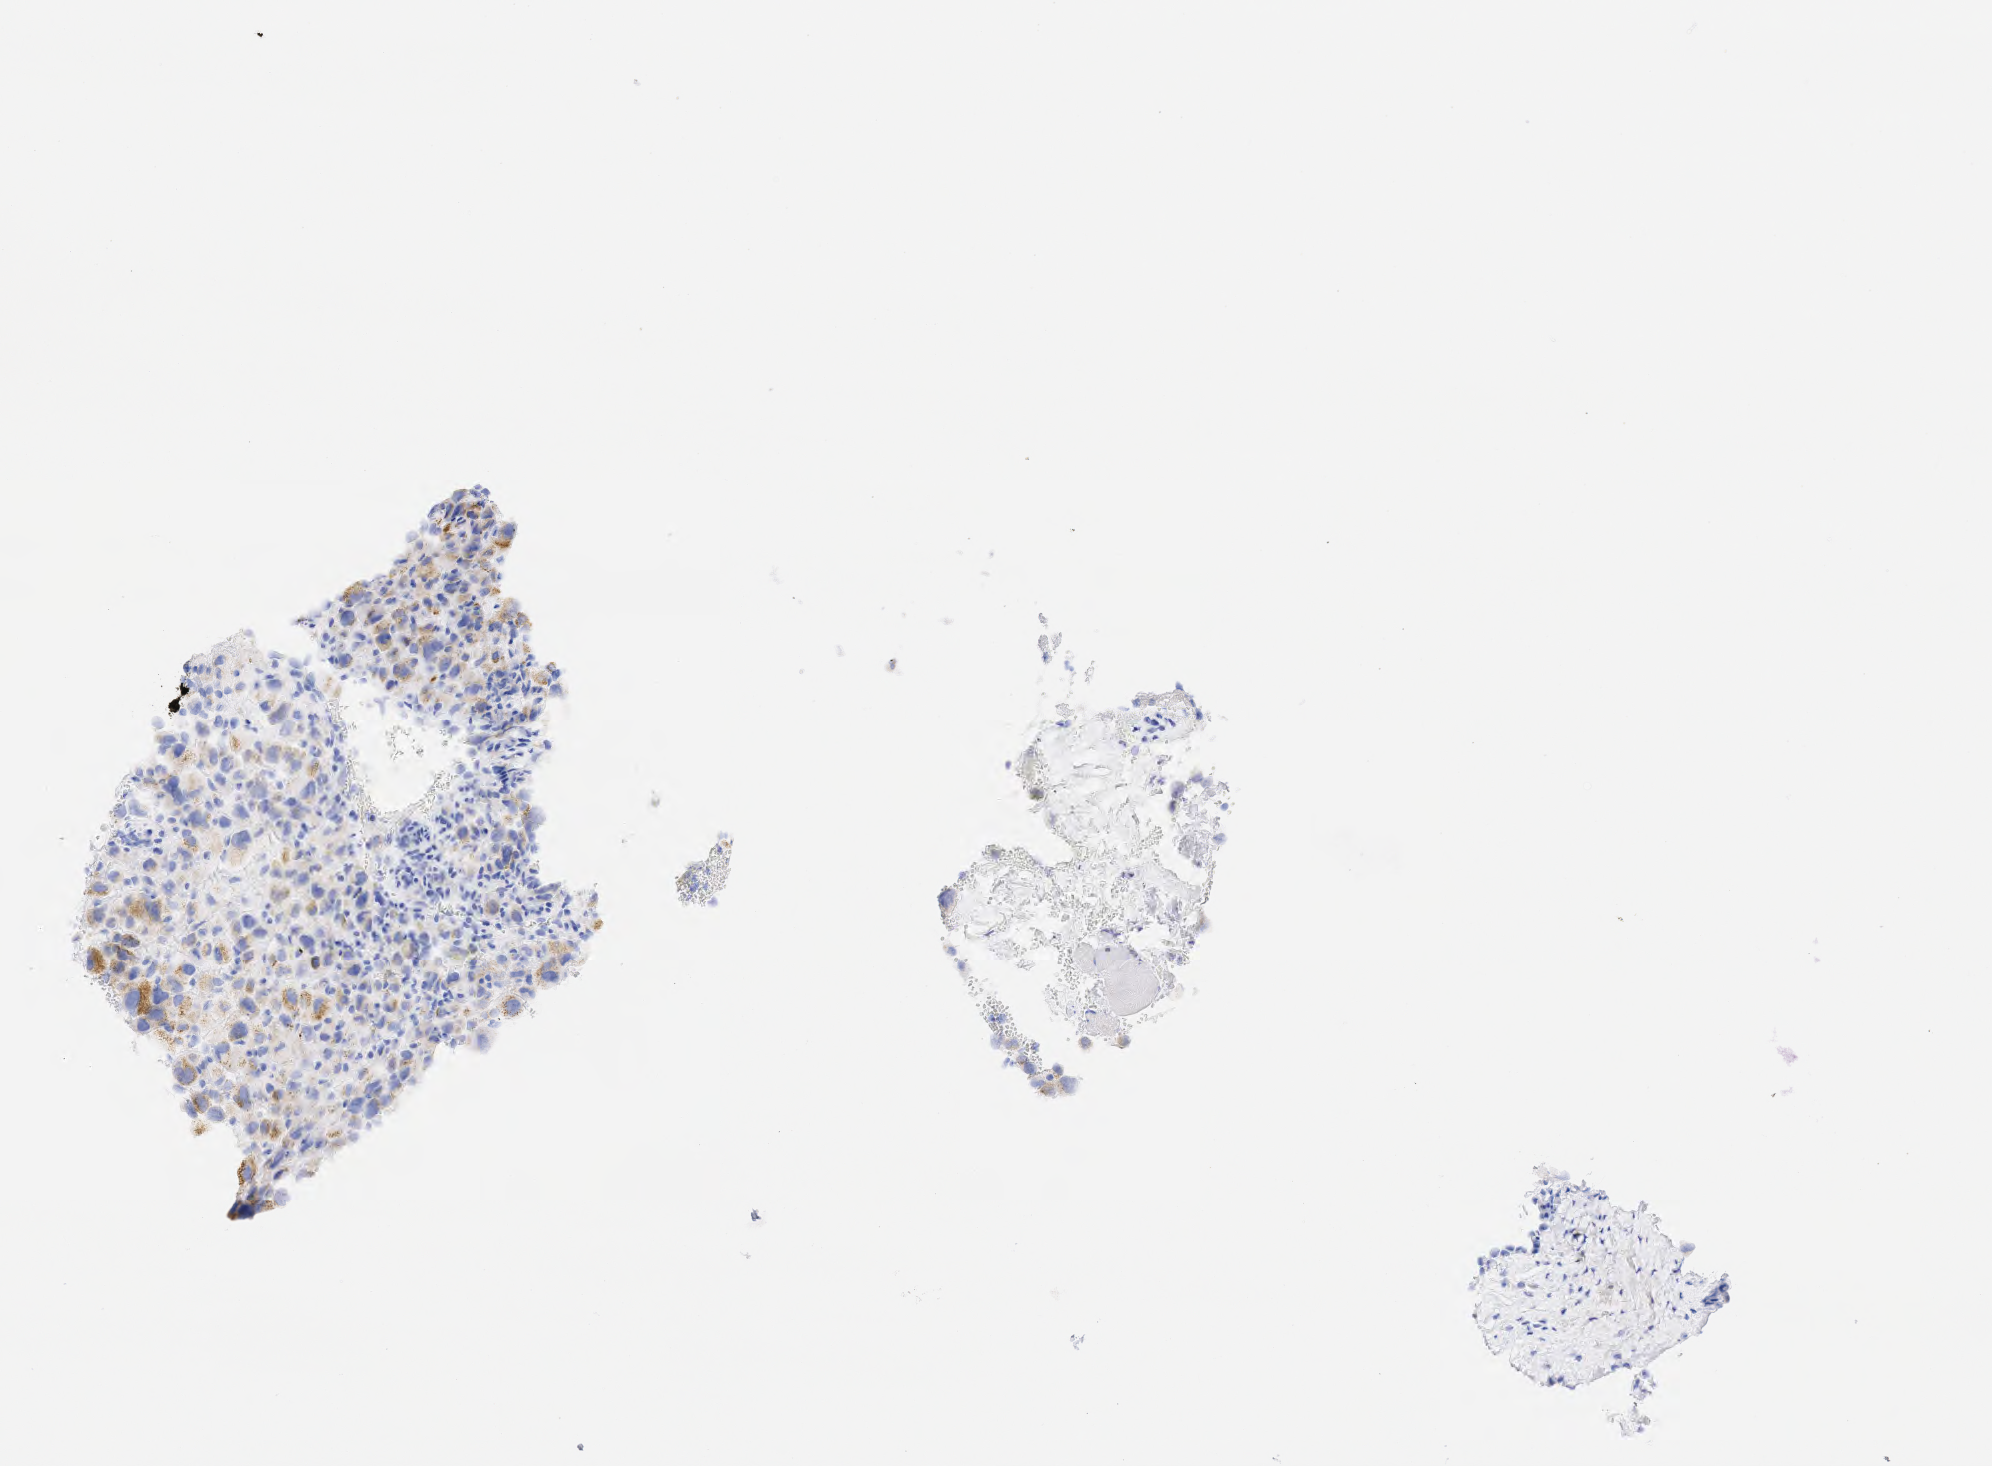
Immunohistochemistry (IHC) whole-slide image stained for p40 — shown as a low-resolution overview of the whole scanned area (about 2.0 x 1.5 mm). Specimen: tumor tissue. Site: lung (right). Male patient, age 63 years.
• histologic diagnosis: Adenocarcinoma, NOS